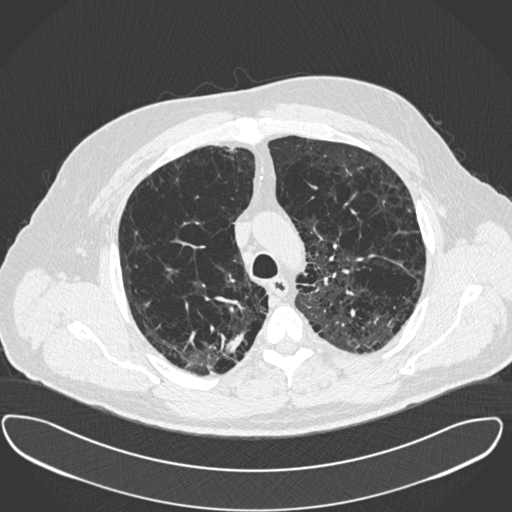
Low-dose screening chest CT, one axial slice; position 292 of 385 along the scan axis; reconstruction kernel B30f; 120 kVp; lung window (W 1500 / L -600 HU); 1 mm slice thickness; 512 × 512 image matrix, field of view 408 × 408 mm.
Structures marked on this image (outlined manually by an expert reader):
- lesion 1 (tumor, upper lobe of right lung): bounding box (x1, y1, x2, y2) in pixels: (226, 332, 245, 353)